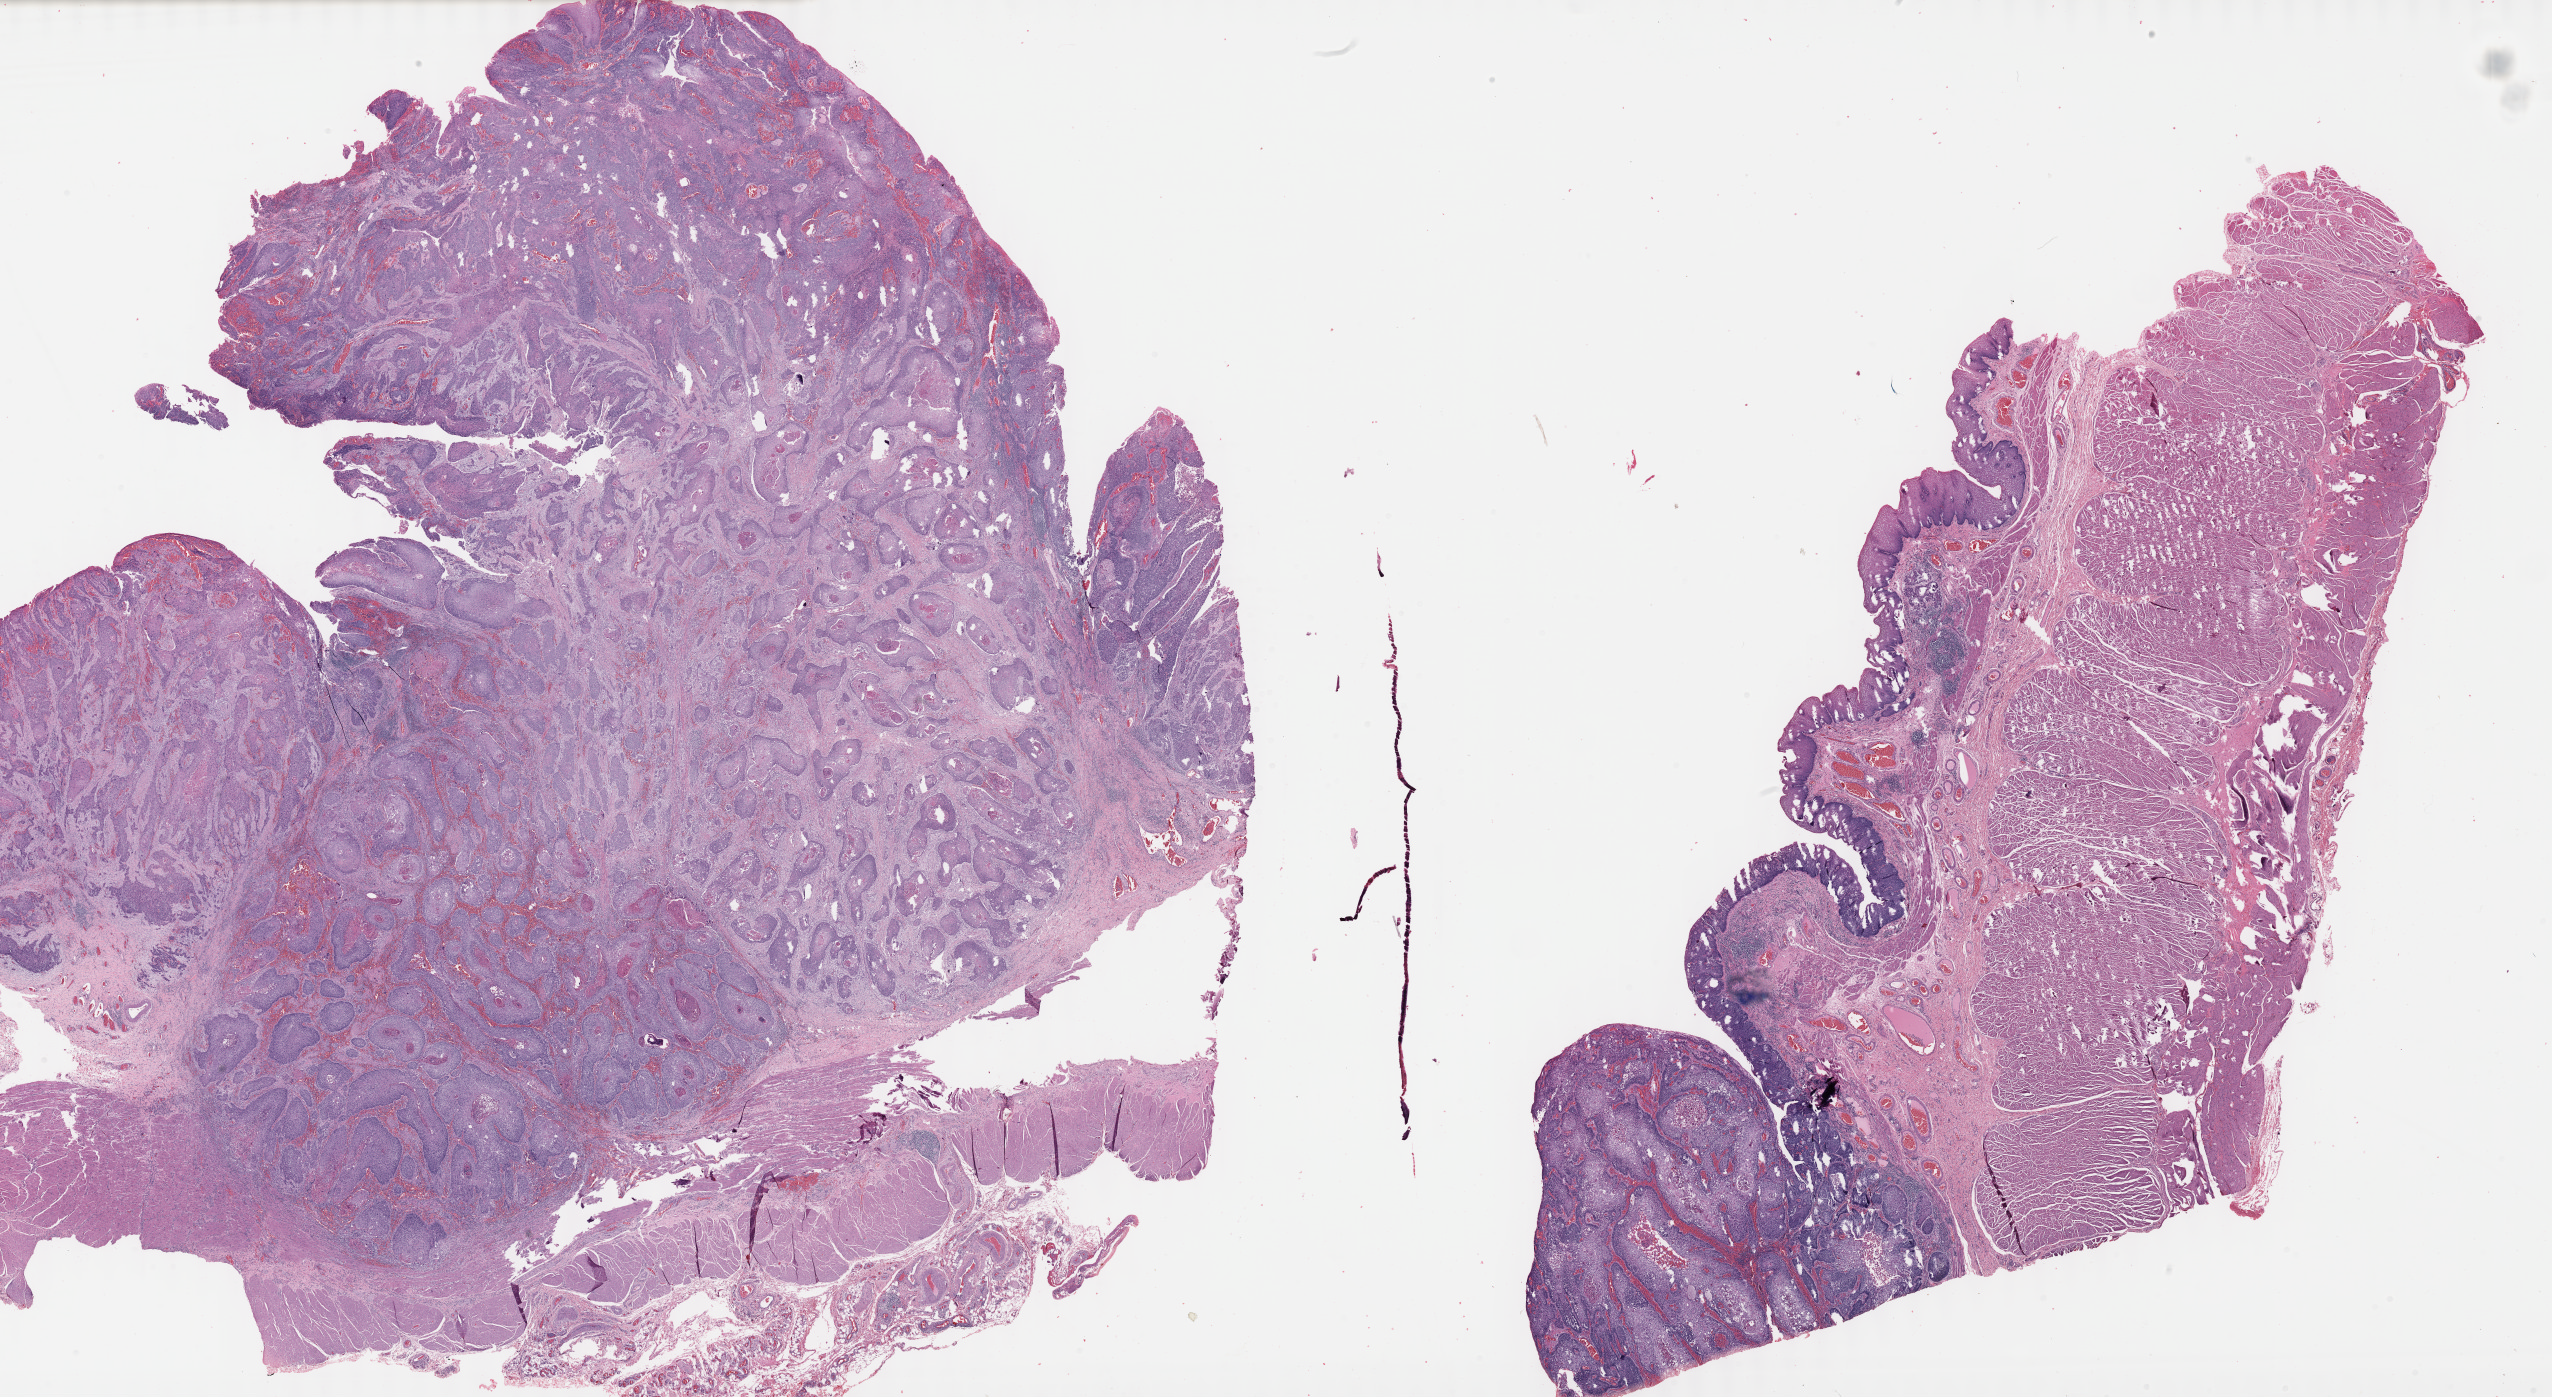
Digitized Hematoxylin and eosin (H&E) stained tissue section (whole slide), low-resolution overview of the scanned area, about 41.2 x 22.6 mm; formalin-fixed paraffin-embedded (FFPE) diagnostic section; sample: primary tumour, esophagus. Male patient; age at initial diagnosis 54 years. Histologic grade: G2 (moderately differentiated).
• AJCC pathologic stage: IIB
• pathologic diagnosis: Squamous cell carcinoma, NOS (lower third of esophagus)